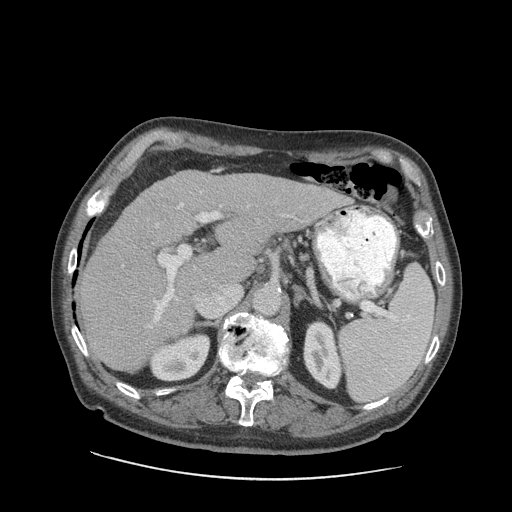
Contrast-enhanced abdominal CT (liver protocol), one axial slice; slice 55 of 89 in the series (ordered by position); reconstruction kernel STANDARD; 140 kVp; soft-tissue window (W 400 / L 40 HU); 2.5 mm slice thickness; 512 × 512 image matrix, field of view 420 × 420 mm. From the clinical record (not read from this slice): diagnosis: hepatocellular carcinoma (patient treated with transarterial chemoembolisation; whether this scan precedes or follows treatment is not stated here); TNM stage (as recorded): Stage-I; Child-Pugh class: A; tumour nodularity: uninodular; tumour size: 4.6 cm.
Outlined on this slice (semi-automatic segmentation, software-assisted and operator-edited):
- liver parenchyma outside the tumour (the mass and vessels are separate outlines, so this box may not span the whole liver): bounding box [x1, y1, x2, y2] px = [78, 170, 342, 372]
- liver vessels: [122, 180, 337, 329]